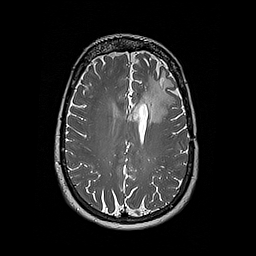
Brain MRI from a brain-tumour surgery series, one axial slice. Position 120 of 192 along the scan axis. 1 mm slice thickness. 256 × 256 image matrix. From the clinical record (not read from this slice): histopathology: Oligodendroglioma; WHO grade: 2; IDH mutation: yes.
Structures marked on this image (expert manual segmentation):
- tumour: box from (x=141, y=76) to (x=173, y=123) px